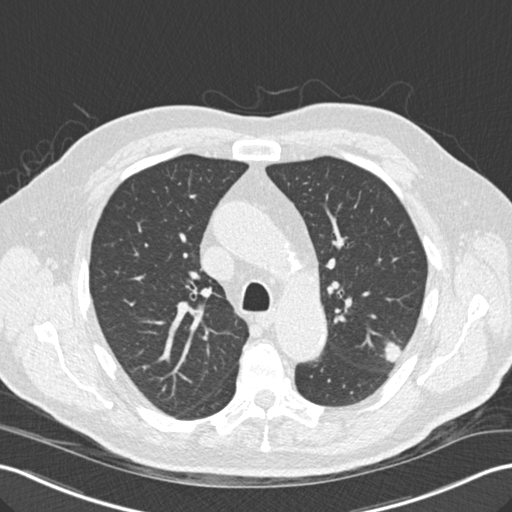
Chest CT (low-dose screening protocol), one axial image. Third annual screen. Lung window (W 1500 / L -600 HU). 2 mm slice thickness. Standard (soft-tissue) reconstruction kernel (B30f). Slice 54 of 157 in the series. 512 × 512 image matrix. Male, age 67 years at enrolment. Former smoker at enrolment.
Lesion marked by an expert reader, bounding box <365,331,413,375> (left, top, right, bottom; pixels). The screening reader recorded 2 non-calcified nodules or masses ≥4 mm on this exam (left upper lobe, left lower lobe); which of them this box marks is not recorded.